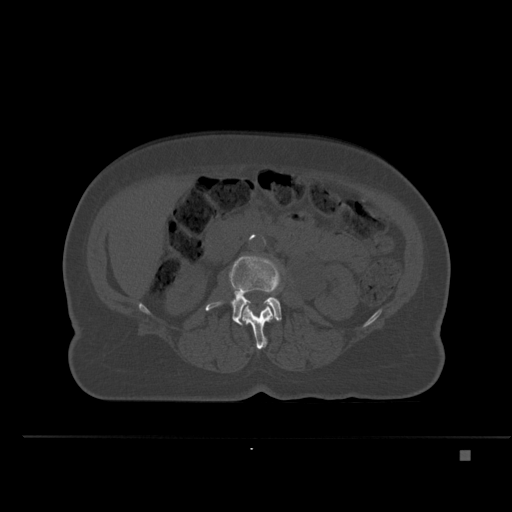
CT including the spine, one axial slice; position 206 of 477 along the scan axis; bone window (W 1800 / L 400 HU); 1.5 mm slice thickness; 512 × 512 image matrix, field of view 422 × 422 mm. Female patient, age 74 years. From the clinical record (not read from this slice): primary cancer: colon.
Outlined on this slice (semi-automatic segmentation, software-assisted and operator-edited):
- L2 vertebra: bounding box [x1, y1, x2, y2] px = [243, 305, 274, 349]
- L3 vertebra: [205, 255, 282, 325]